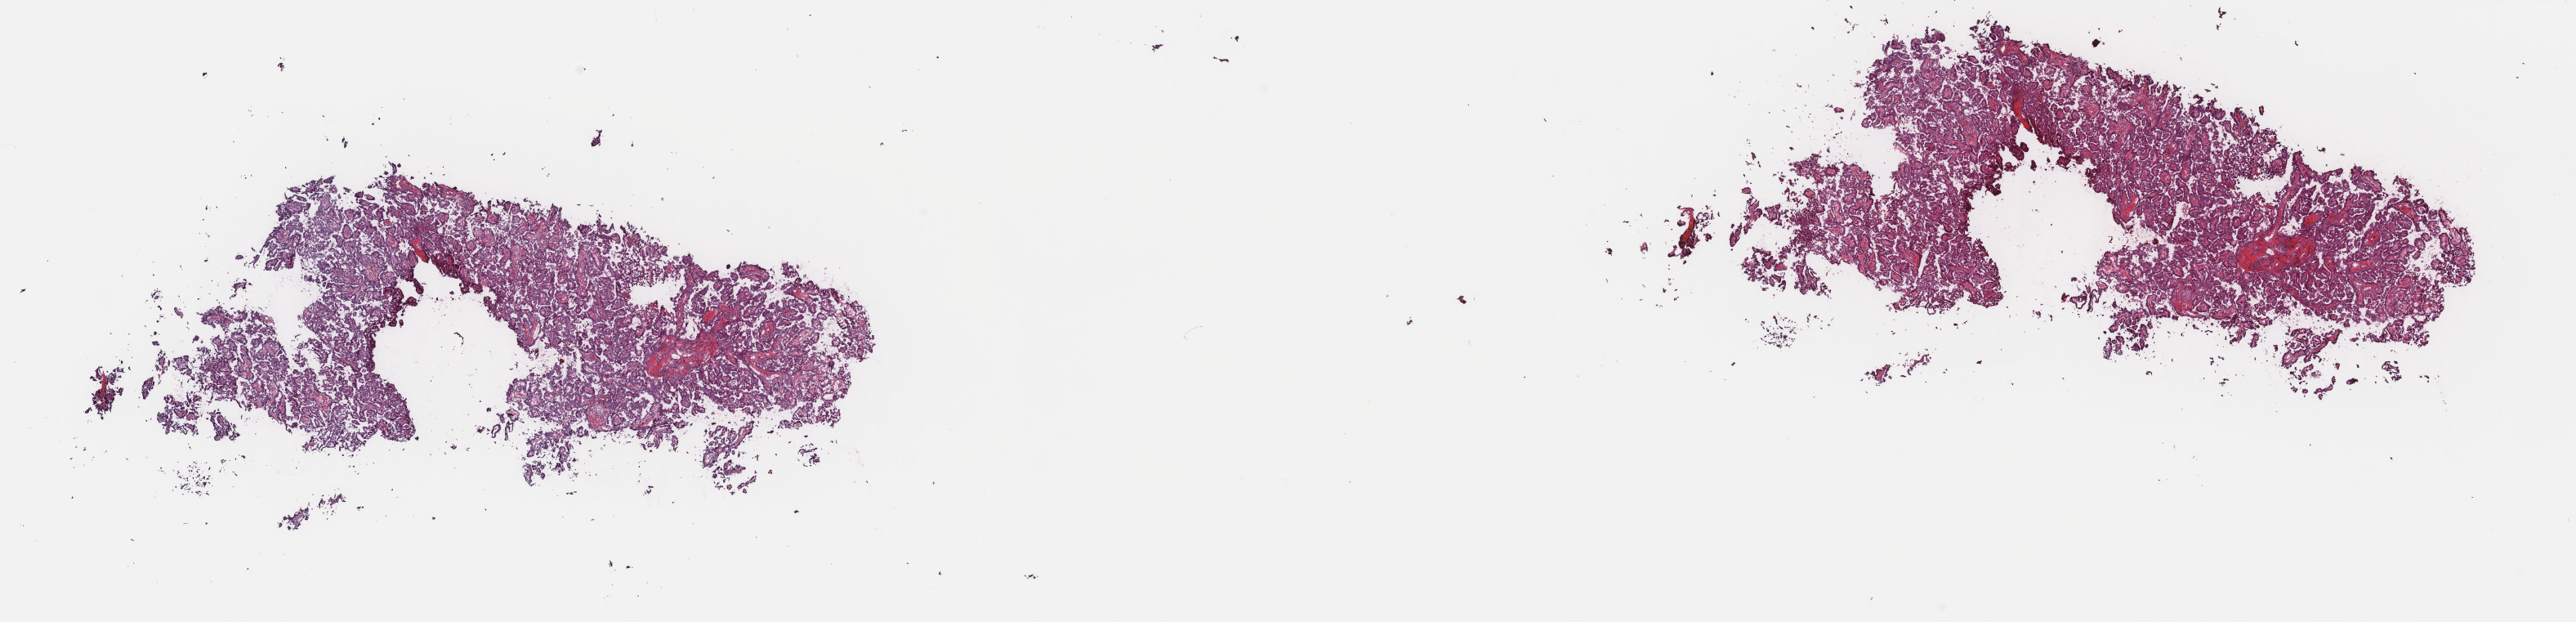
Whole-slide histology image, H&E, whole scanned area (about 25.0 x 6.0 mm, from a 40x scan) shown as a low-resolution overview, frozen section, primary tumour sample from the thyroid. Patient: male, age at initial diagnosis 24 years. Composition of this section per pathologist review: tumour cells 90%, tumour nuclei 90%, normal cells 0%, stromal cells 10%, necrosis 0%. Infiltration values recorded for this section: lymphocyte infiltration 2%, monocyte infiltration 1%, neutrophil infiltration 0%.
Pathologic diagnosis: Papillary adenocarcinoma, NOS (thyroid gland). AJCC pathologic stage: I. Lymph nodes positive (case pathology): 1 of 4 examined.